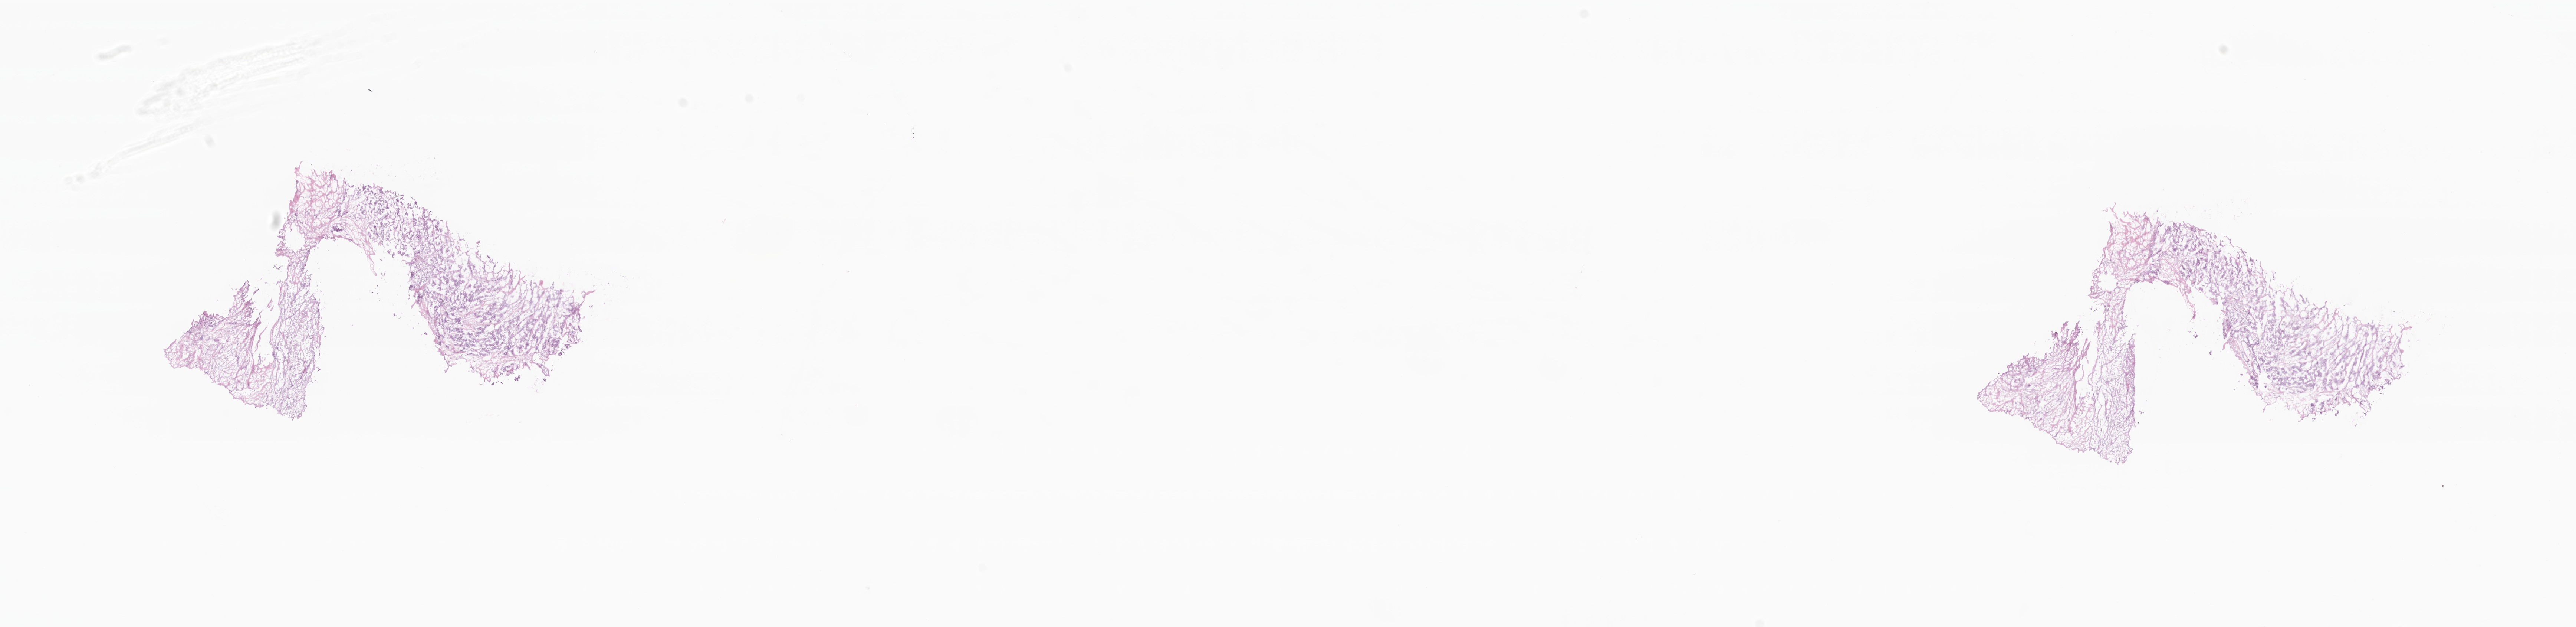
Whole-slide image, H&E stain — low-resolution overview of the scanned area, about 29.3 x 7.1 mm. Frozen section (tissue freezing medium). Primary tumor. Site: breast (right). Female, age 61 years at initial diagnosis. Pathologist review of this section (percent, as recorded): tumor cells 50%, tumor nuclei 95%, stromal cells 50%, necrosis 0%, normal cells 0%. Inflammatory infiltration, as recorded: lymphocyte infiltration 0%, monocyte infiltration 0%, neutrophil infiltration 0%.
* section: bottom of the tissue portion
* diagnosis: Infiltrating duct carcinoma, NOS